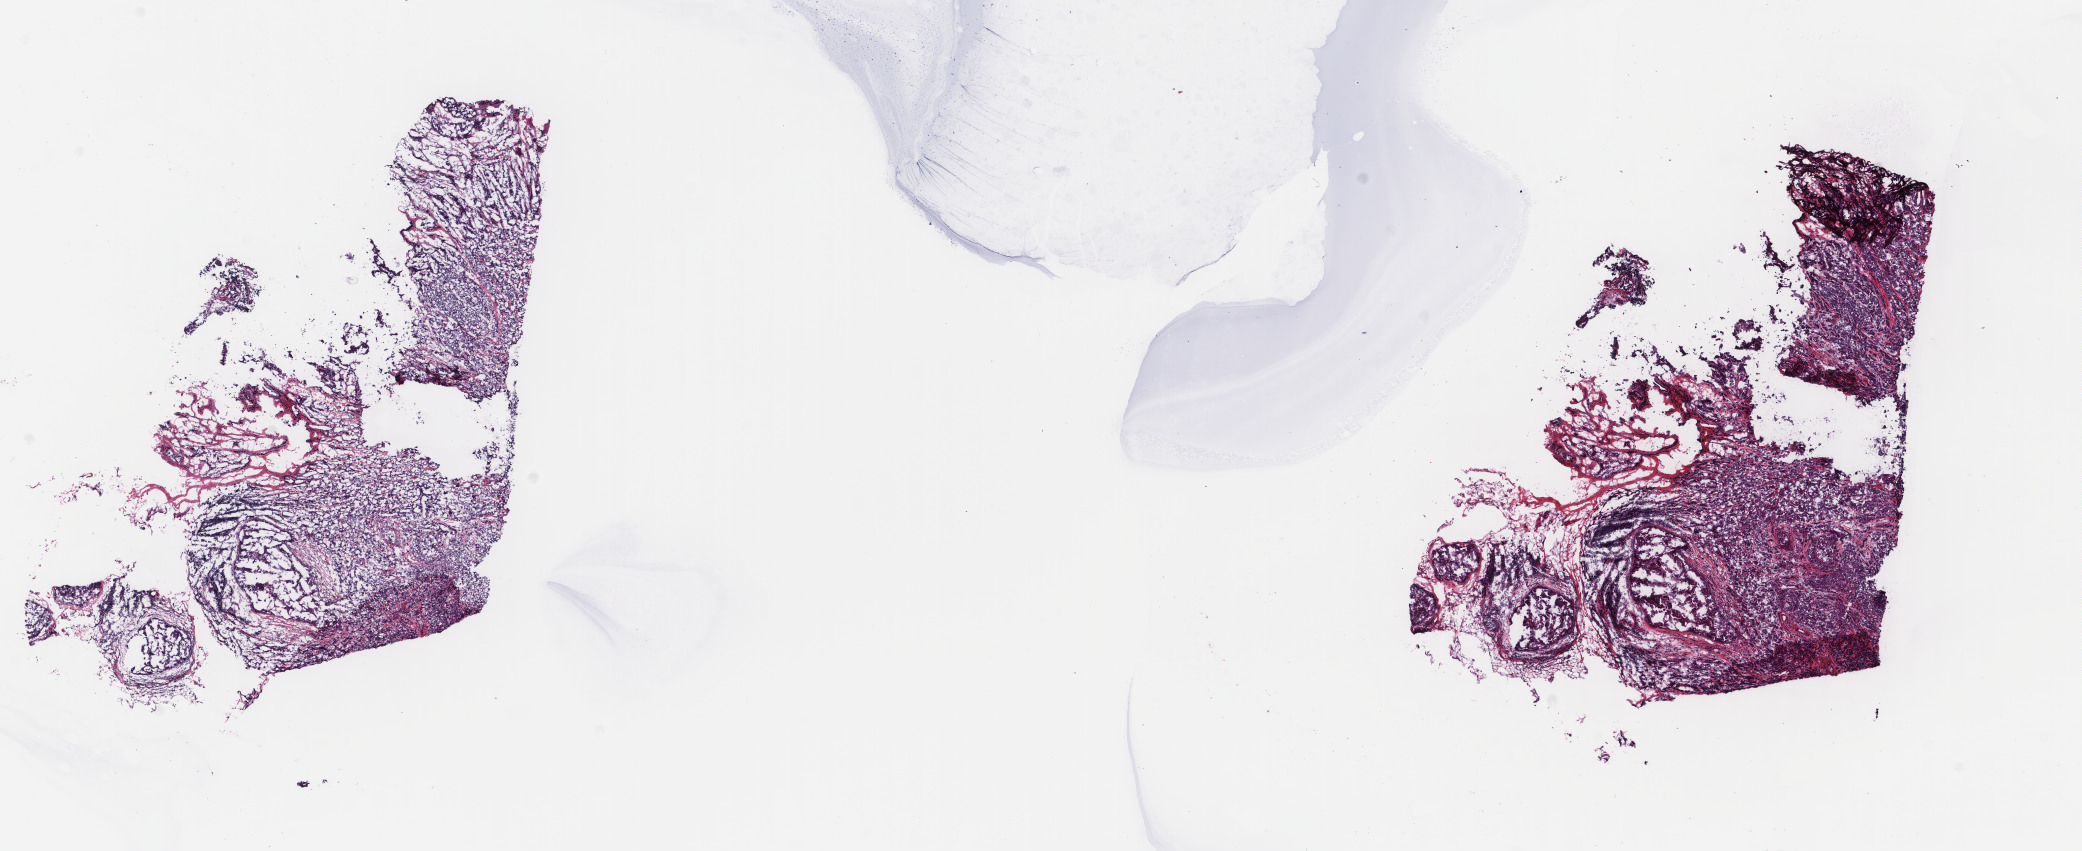
Whole-slide histology image, H&E-stained, low-resolution overview of the scanned area, about 16.5 x 6.8 mm (from a 40x scan), frozen section, sample: primary tumour, breast. Female patient; age at initial diagnosis 34 years. Pathologist review of this section (percent, as recorded): tumour cells 72%, tumour nuclei 85%, normal cells 0%, stromal cells 26%, necrosis 2%. Inflammatory infiltration, as recorded: lymphocyte infiltration 5%, monocyte infiltration 0%, neutrophil infiltration 0%.
AJCC pathologic stage: IIIA (6th edition). Laterality: left. Histologic diagnosis: Infiltrating duct carcinoma, NOS.